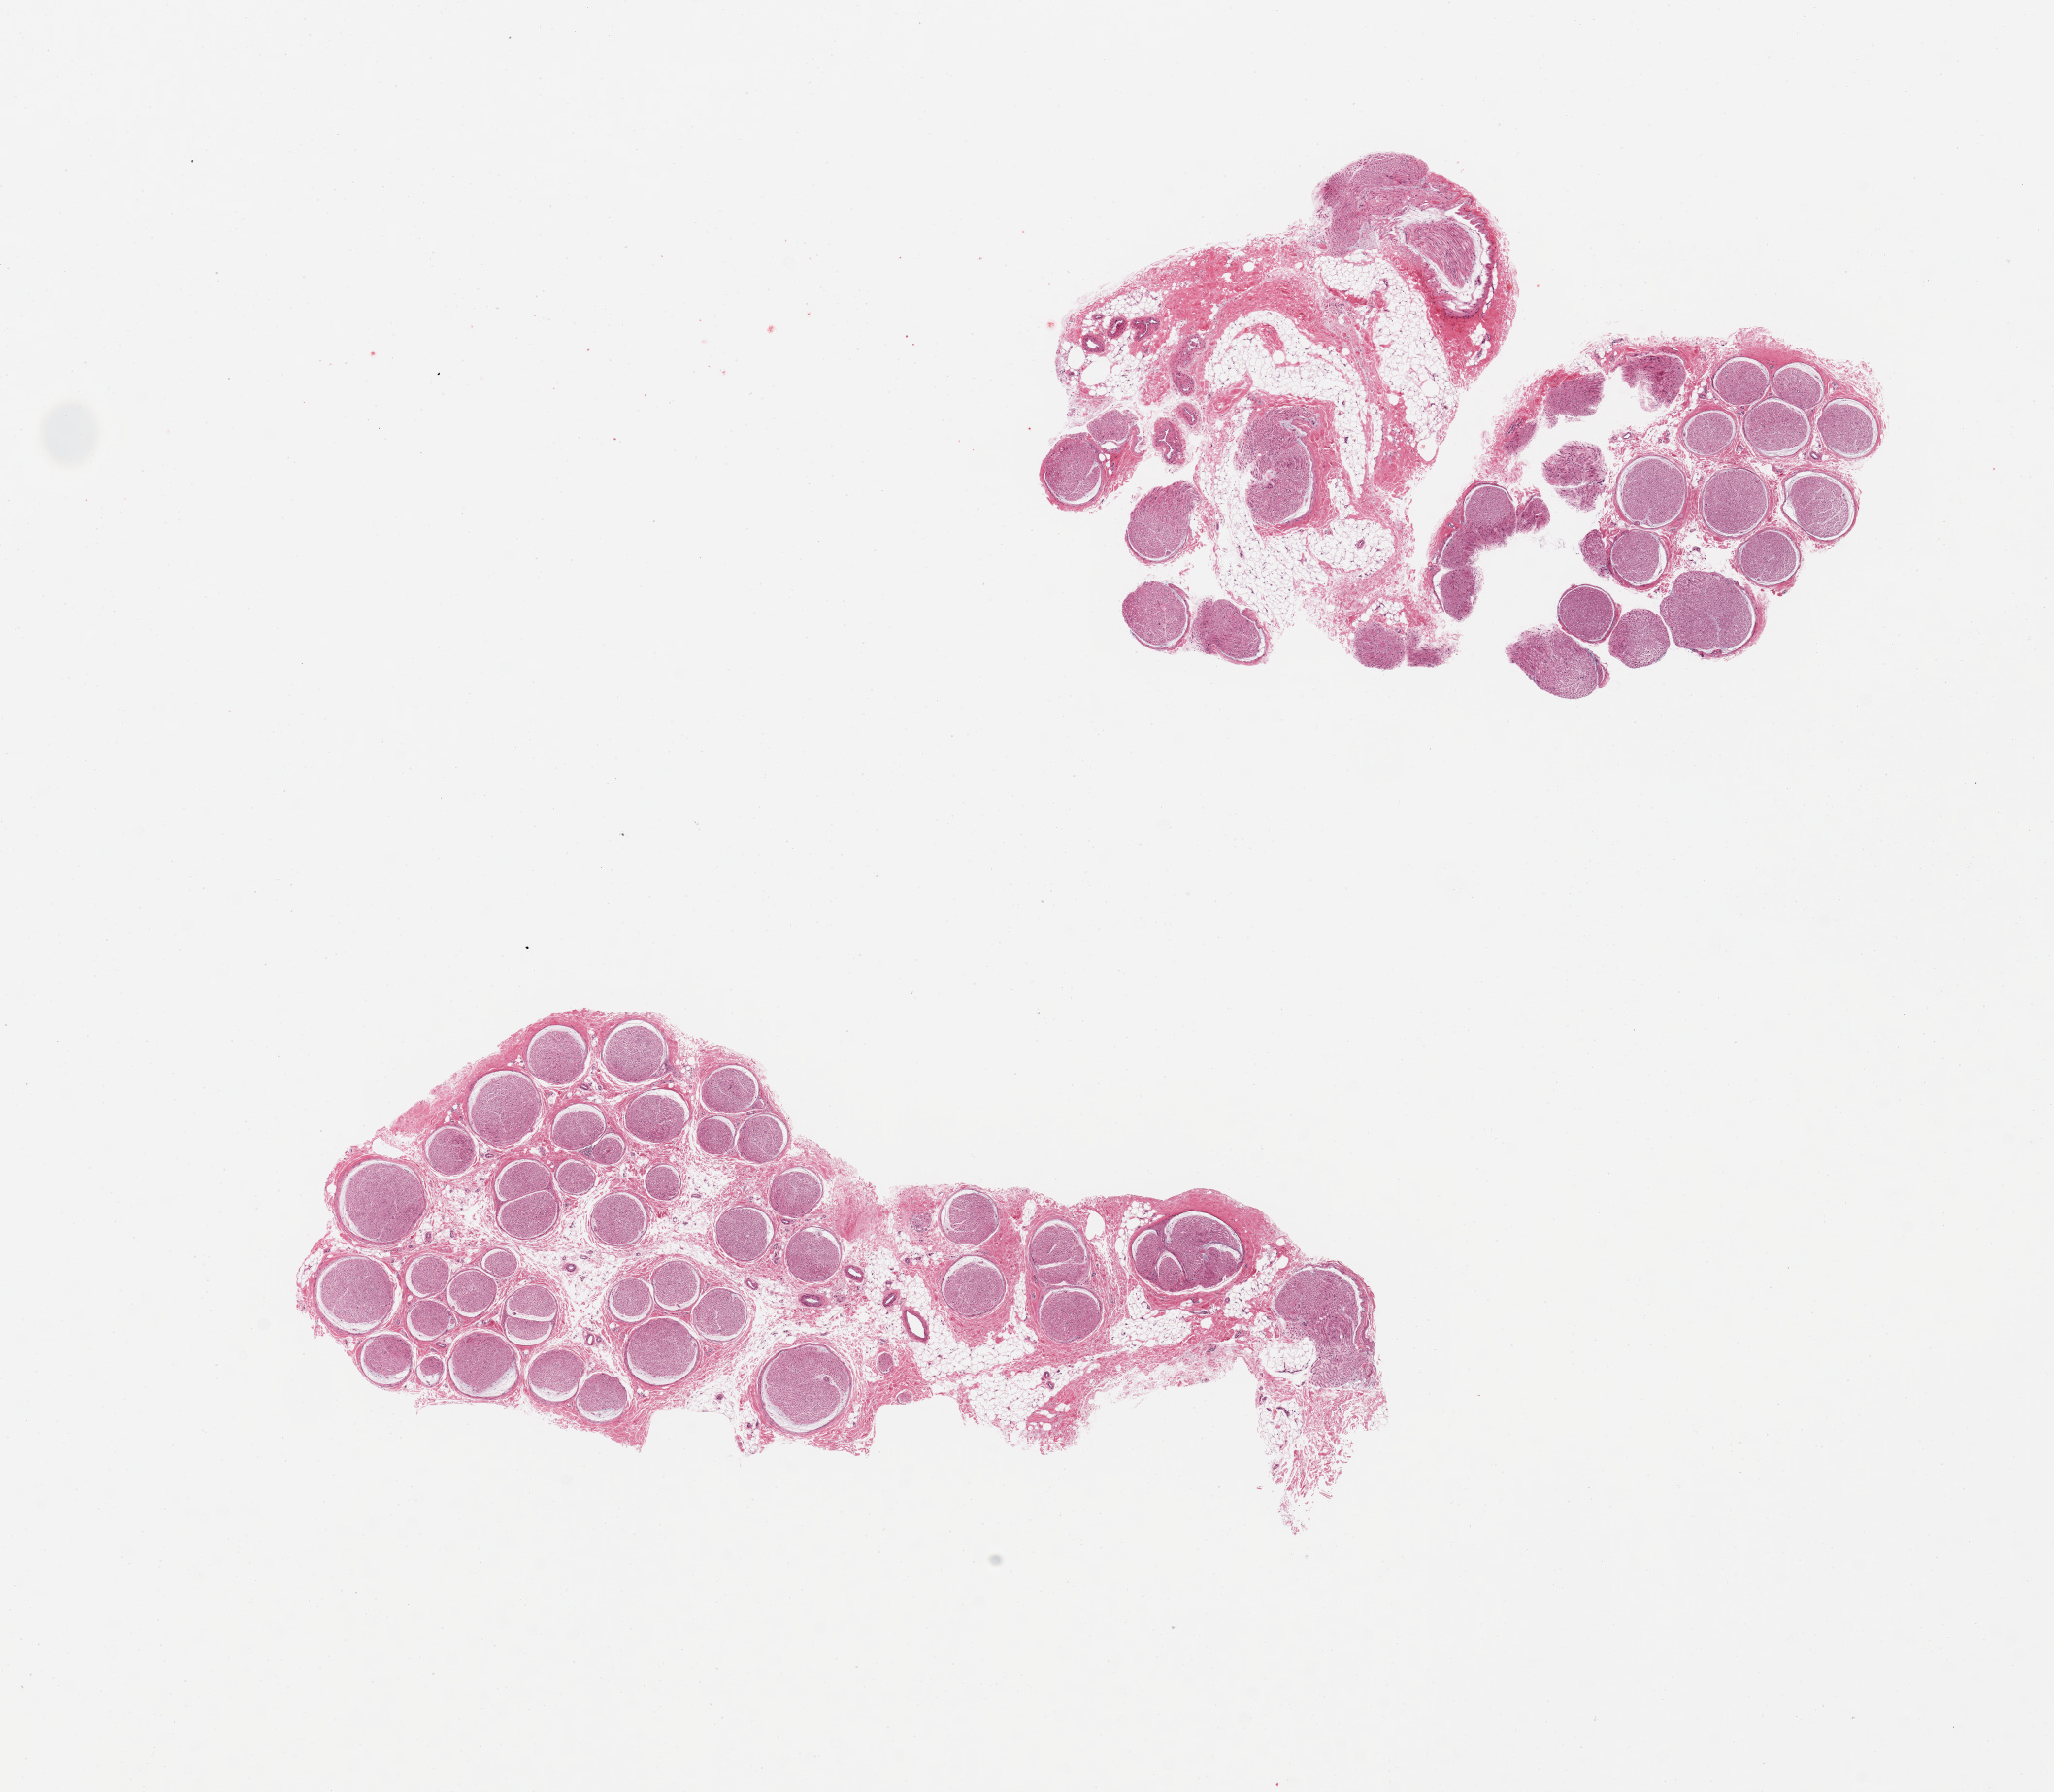
Whole-slide image, hematoxylin and eosin (H&E) stain — a low-resolution overview of the entire scanned area, about 16.7 x 14.6 mm (slide scanned at 20x), PAXgene-fixed paraffin-embedded (PFPE) section, sampled site (target tissue): tibial nerve, tissue donor sample. Female donor.
* pathologist's review note for this sample: 2 pieces, 10-30% fat and fibrous tissue